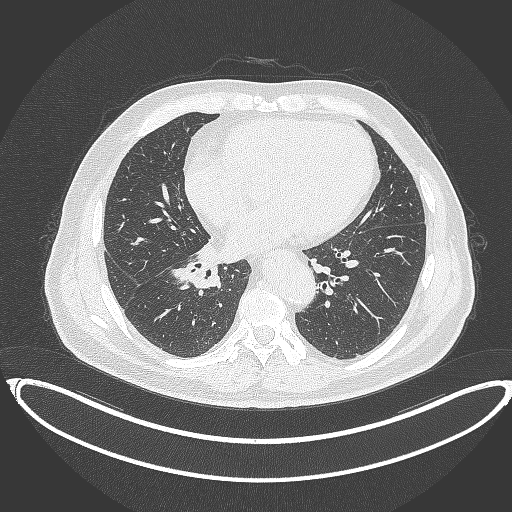
Chest CT, one axial slice. Reconstruction kernel B70f. 120 kVp. Lung window (W 1500 / L -600 HU). 1 mm slice thickness. 512 × 512 image matrix. Male patient, age 61 years. Case-level facts recorded for this patient, not image findings: clinical TNM (as recorded): T1b N1 M0.
Outlined on this slice (rectangle marked by the reading radiologist):
- lung tumour (recorded histology: squamous cell carcinoma): box from (x=172, y=260) to (x=220, y=289) px